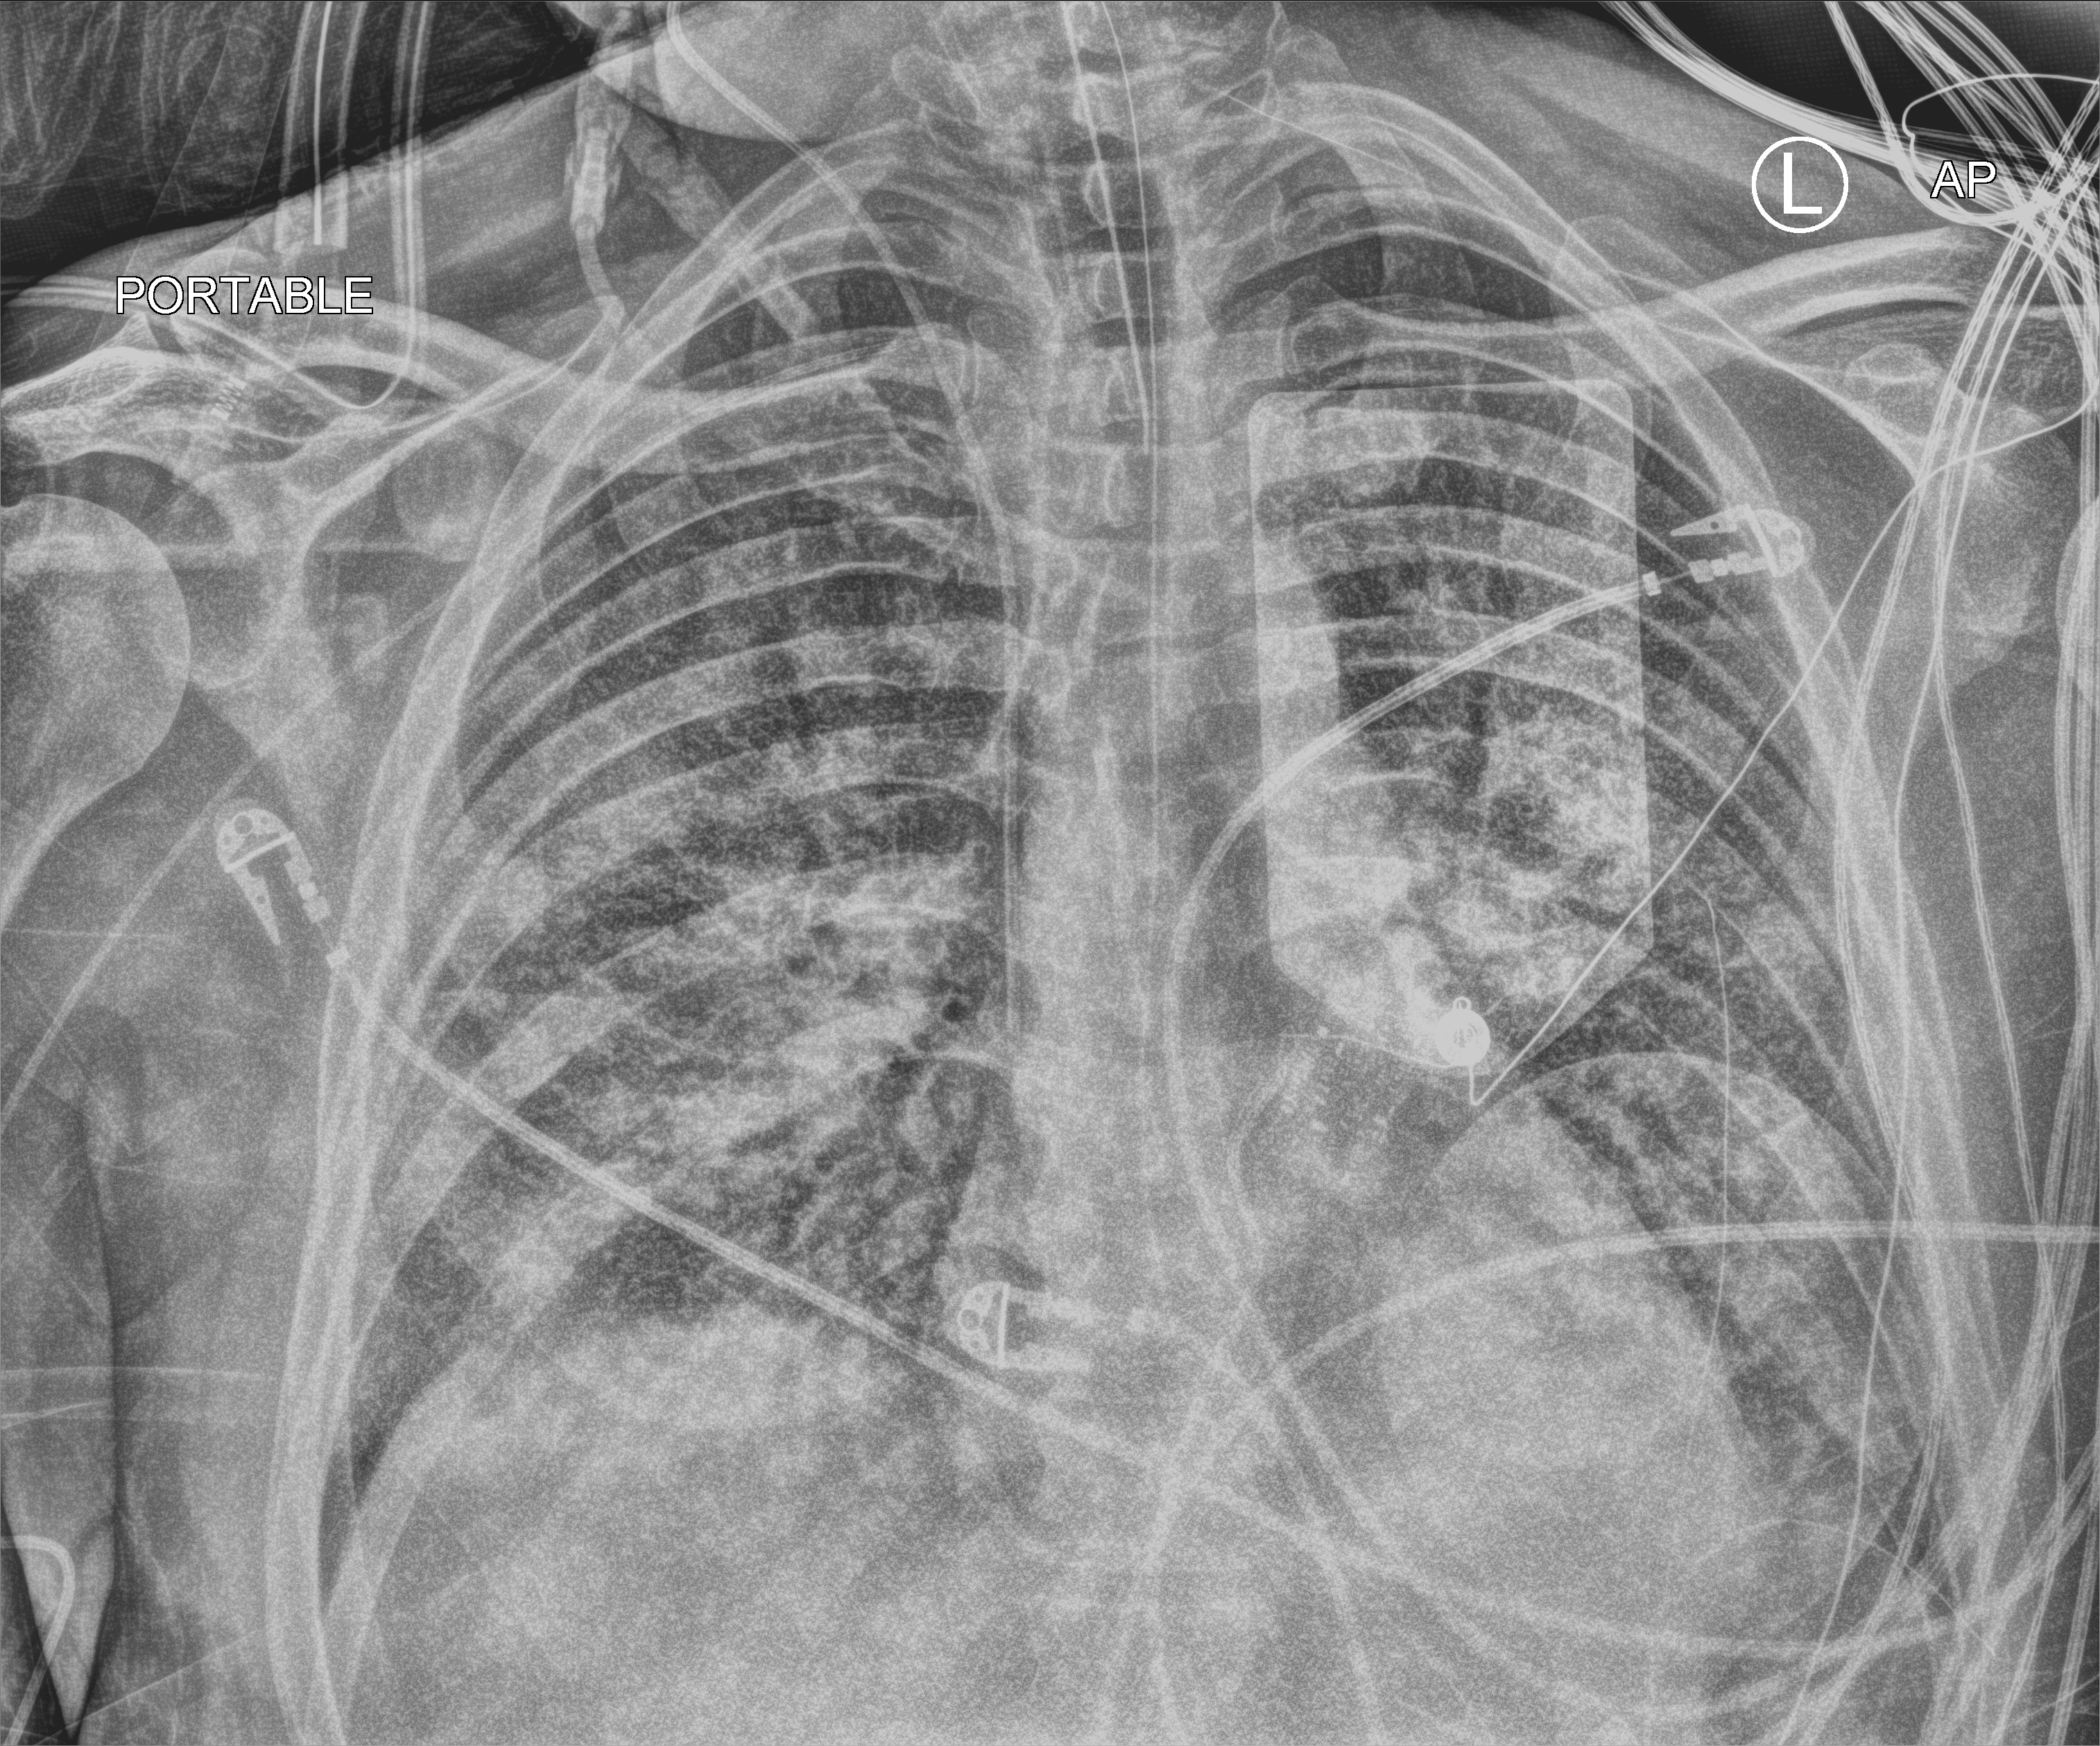
Bedside chest radiograph (computed radiography); anteroposterior (AP) projection. Male patient hospitalised with COVID-19, age 18–59 years.
Hospital-stay facts (about this admission, not read from this image; timing relative to this image not recorded): diabetes (admission record): no; admitted to intensive care during this hospital stay: yes.